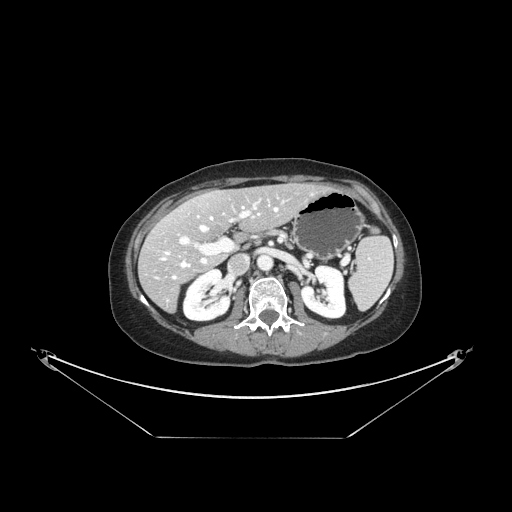
Contrast-enhanced abdominal CT, one axial slice. Position 80 of 148 along the scan axis. Soft-tissue window (W 400 / L 40 HU). 512 × 512 image matrix, field of view 500 × 500 mm. Female patient, age 73 years. Case-level facts recorded for this patient, not image findings: diagnosis: colorectal cancer liver metastases, imaged before liver resection; multiple liver metastases: no; largest metastasis: 1 cm; disease in both lobes: no.
Outlined on this slice (manually delineated by an expert):
- hepatic veins: box from (x=162, y=204) to (x=279, y=279) px
- liver: (x=139, y=184)–(x=325, y=311)
- planned liver remnant (the part of the liver to remain after resection): (x=168, y=184)–(x=324, y=238)
- portal vein (with intrahepatic branches): (x=179, y=204)–(x=257, y=264)